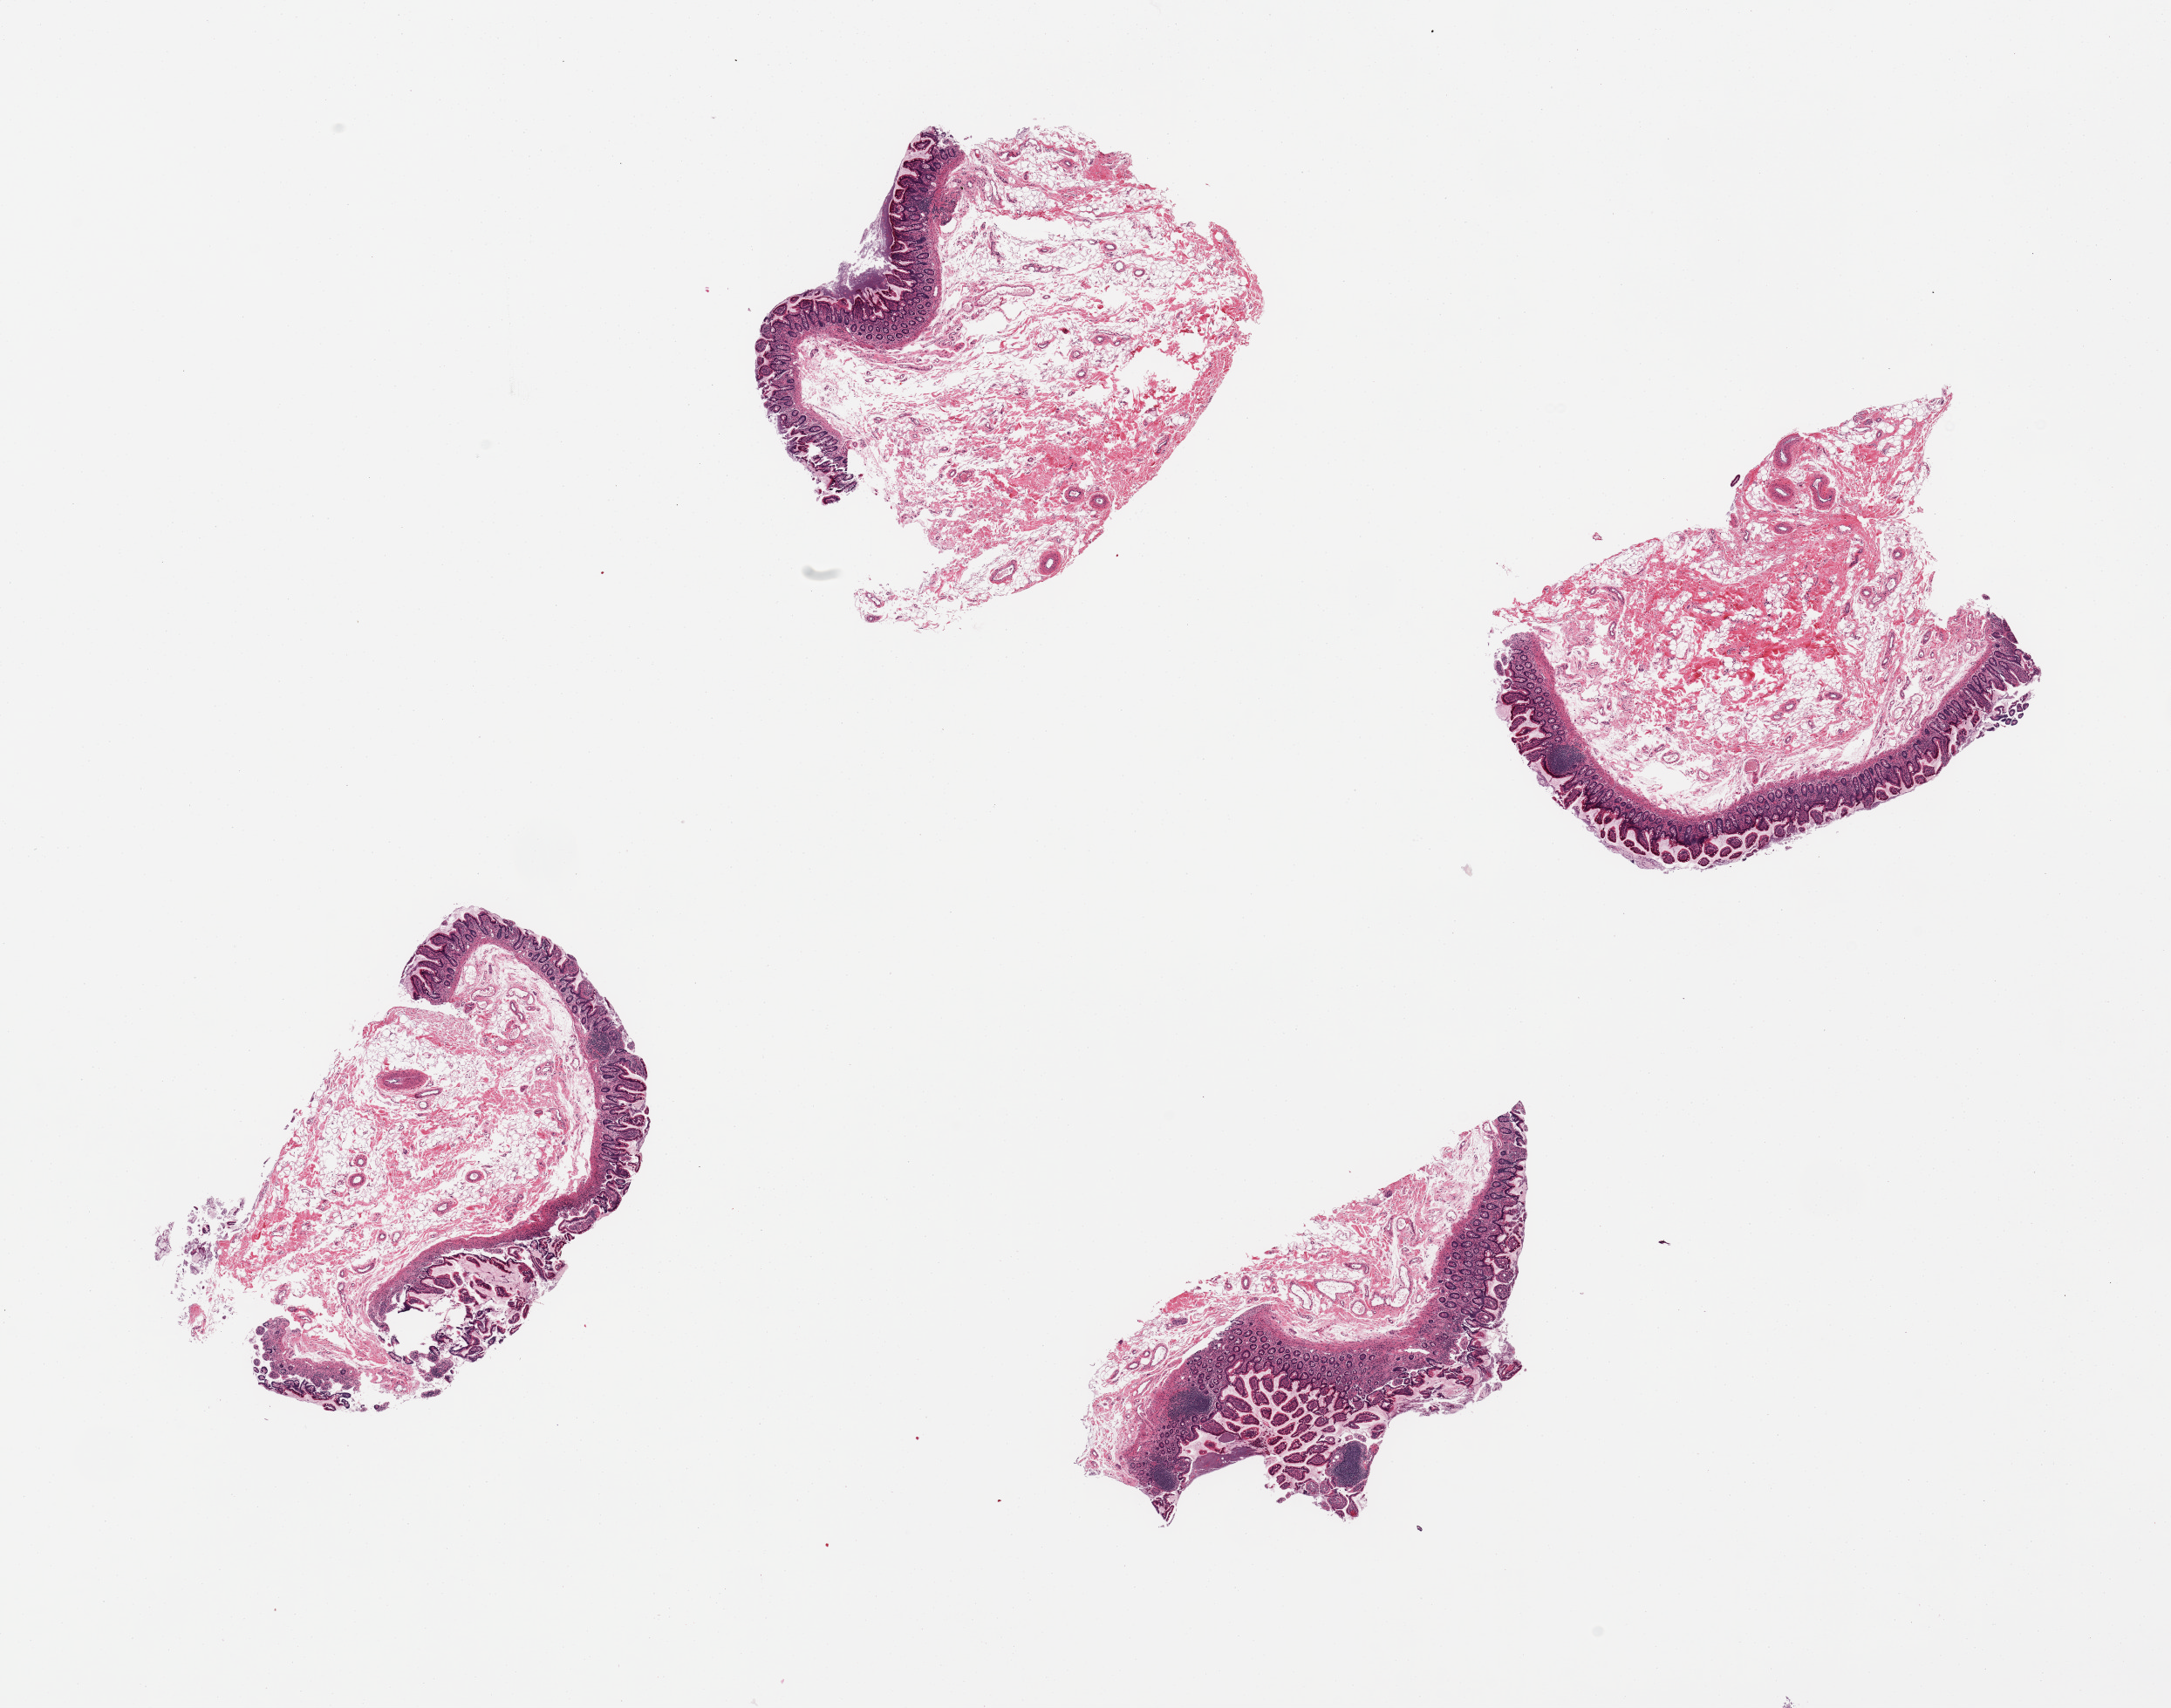
Whole-slide image, hematoxylin and eosin (H&E) stain — a low-resolution overview of the entire scanned area, about 19.7 x 15.5 mm (slide scanned at 20x); PAXgene-fixed, paraffin-embedded tissue; target tissue: ileum; tissue donor sample. Donor sex: male.
• review note (as recorded): 4 pieces, well fixed mucosa but too few lymphoid aggegates to justify analysis